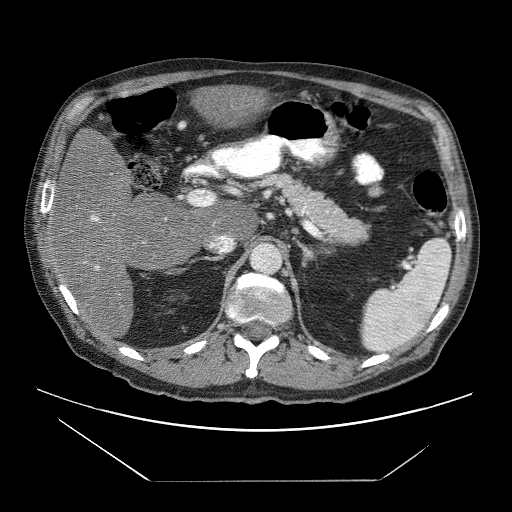
Contrast-enhanced abdominal CT (liver protocol), one axial slice. Position 33 of 83 along the scan axis. 120 kVp. Soft-tissue window (W 400 / L 40 HU). 512 × 512 image matrix, field of view 420 × 420 mm. From the clinical record (not read from this slice): diagnosis: hepatocellular carcinoma (patient treated with transarterial chemoembolisation; whether this scan precedes or follows treatment is not stated here); TNM stage (as recorded): Stage-IVB; Child-Pugh class: B; tumour differentiation: poorly differentiated.
Structures marked on this image (semi-automatic segmentation, software-assisted and operator-edited):
- liver parenchyma outside the tumour (the mass and vessels are separate outlines, so this box may not span the whole liver): bounding box [x1, y1, x2, y2] px = [48, 85, 267, 336]
- liver vessels: [52, 191, 99, 270]